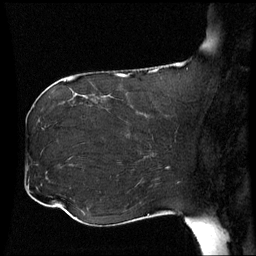
Breast MRI (dynamic contrast-enhanced), one sagittal slice. Position 25 of 60 along the scan axis. Dynamic contrast-enhanced series, image 2 of 3 at this slice position (ordered by acquisition). 1.5 T. TE 4.2 ms, TR 8.9 ms. 256 × 256 image matrix, field of view 230 × 230 mm. Female patient, age 42 years. Case-level facts recorded for this patient, not image findings: setting: breast cancer imaged before/during neoadjuvant chemotherapy; receptor status: HER2-positive.
Structures marked on this image (semi-automatically segmented with operator editing):
- analysis volume of interest (the breast-tissue region the enhancement analysis was run in; not a lesion): bounding box <106,102,173,150> (left, top, right, bottom; pixels)
- tumour enhancement mask (voxels above the 70 % enhancement threshold inside the analysis volume of interest): <140,112,147,117>